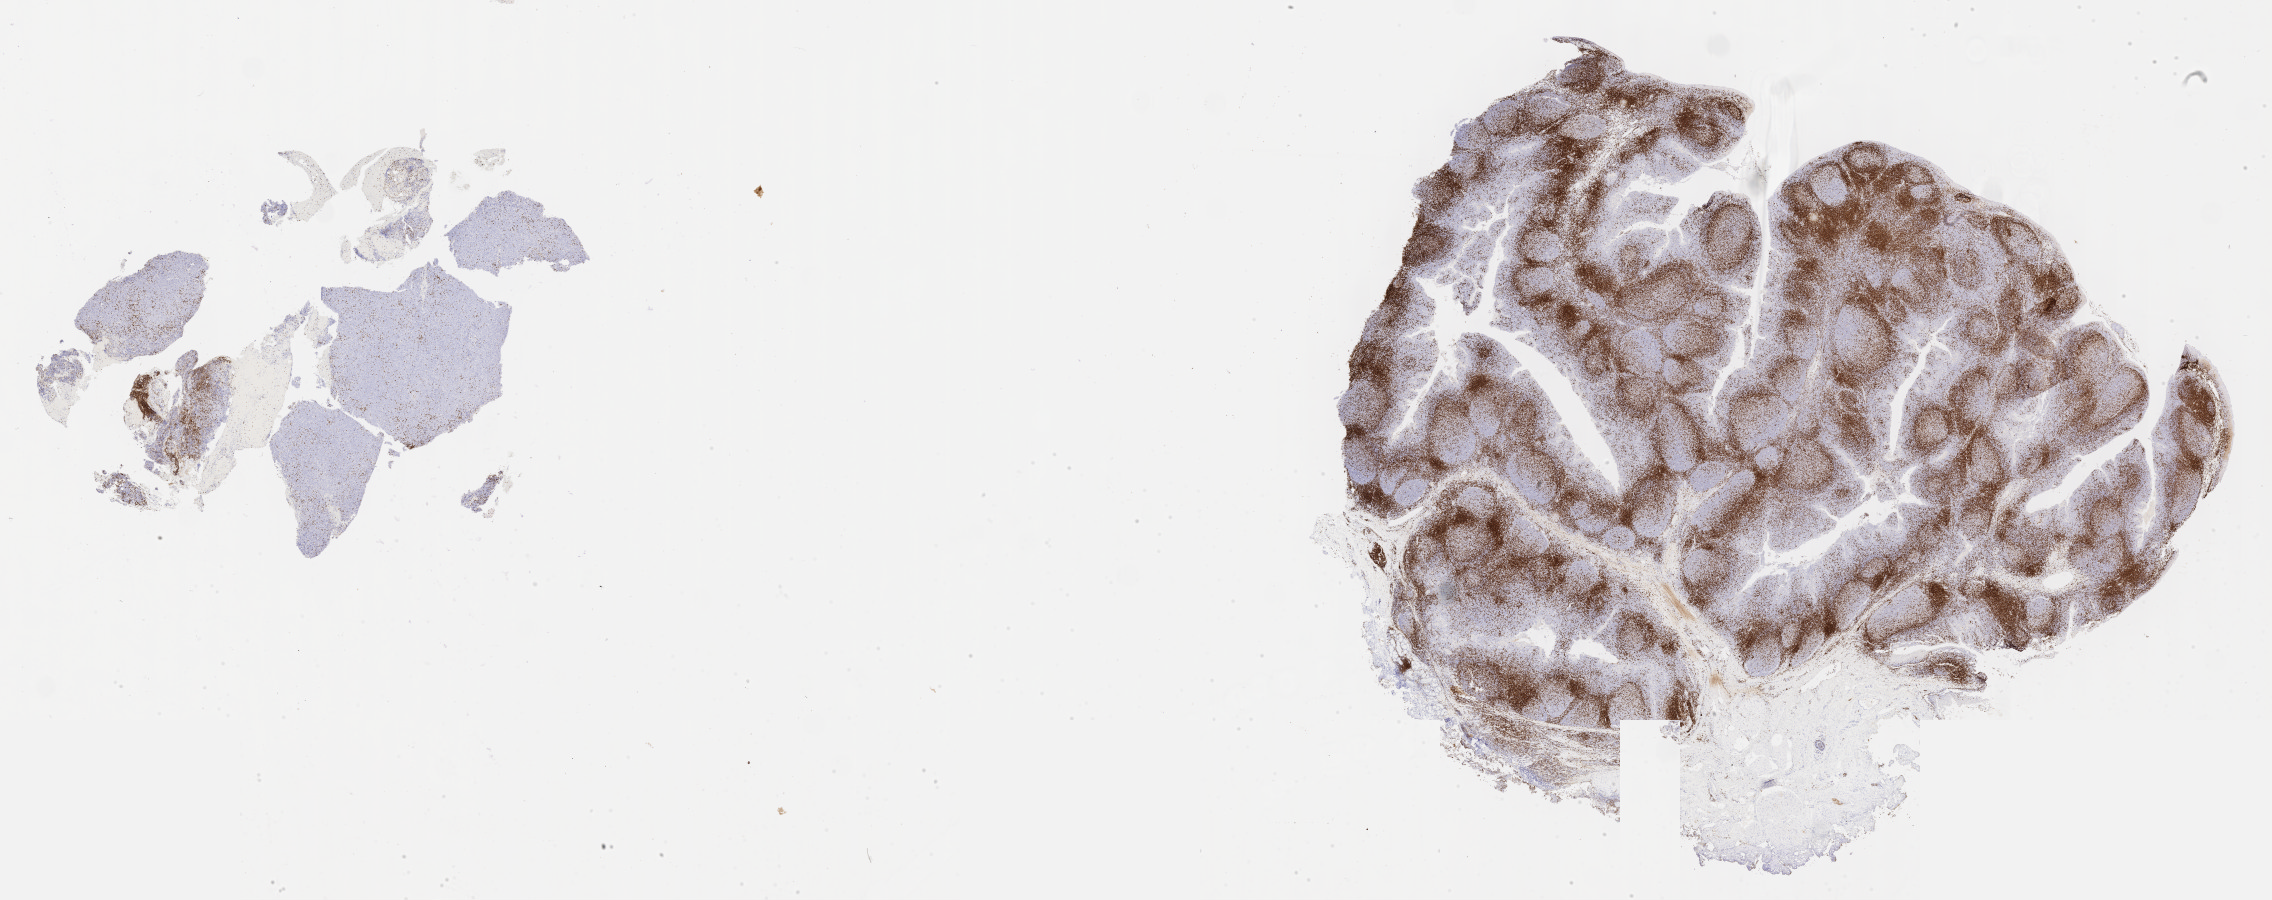
IHC for CD3, whole-slide image — whole scanned area (about 36.7 x 14.6 mm) shown as a low-resolution overview; specimen: tumor tissue; site: lymph node. Patient female; age 71 years.
Histologic diagnosis: Diffuse large B-cell lymphoma, NOS.